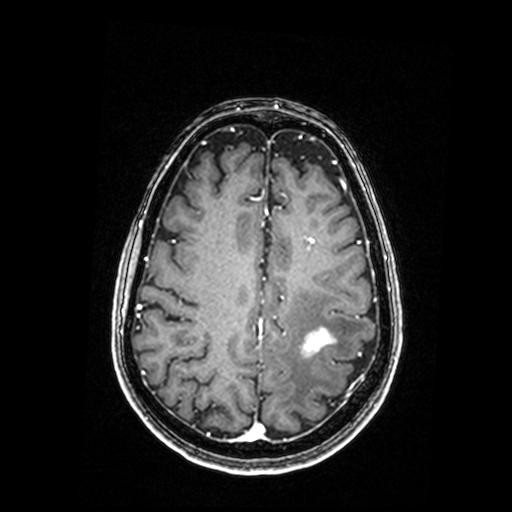
Brain MRI from a brain-tumour surgery series, one axial slice. Position 64 of 192 along the scan axis. T1-weighted post-contrast. 0.98 mm slice thickness. 512 × 512 image matrix, field of view 250 × 250 mm. From the clinical record (not read from this slice): histopathology: Metastastic Carcinoma, Poorly Differentiated; tumour location: Left Parietal.
Annotated regions visible in this slice (expert manual segmentation):
- tumour: bounding box <305,330,333,351> (left, top, right, bottom; pixels)